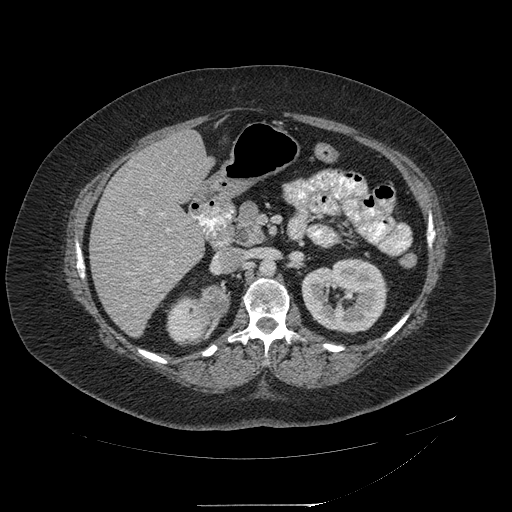
Contrast-enhanced abdominal CT, one axial slice; slice 111 of 217 in the series (ordered by position); reconstruction kernel STANDARD; 120 kVp; intravenous contrast given; soft-tissue window (W 400 / L 40 HU); 1.25 mm slice thickness; 512 × 512 image matrix. Female patient, age 55 years. From the clinical record (not read from this slice): diagnosis: adrenocortical carcinoma; tumour side: right adrenal; tumour size at pathology: 11 cm; Ki-67 index: 20 %; stage (as recorded): 2.
Annotated regions visible in this slice (semi-automatically segmented with operator editing):
- mass: bounding box <201,287,227,317> (left, top, right, bottom; pixels)